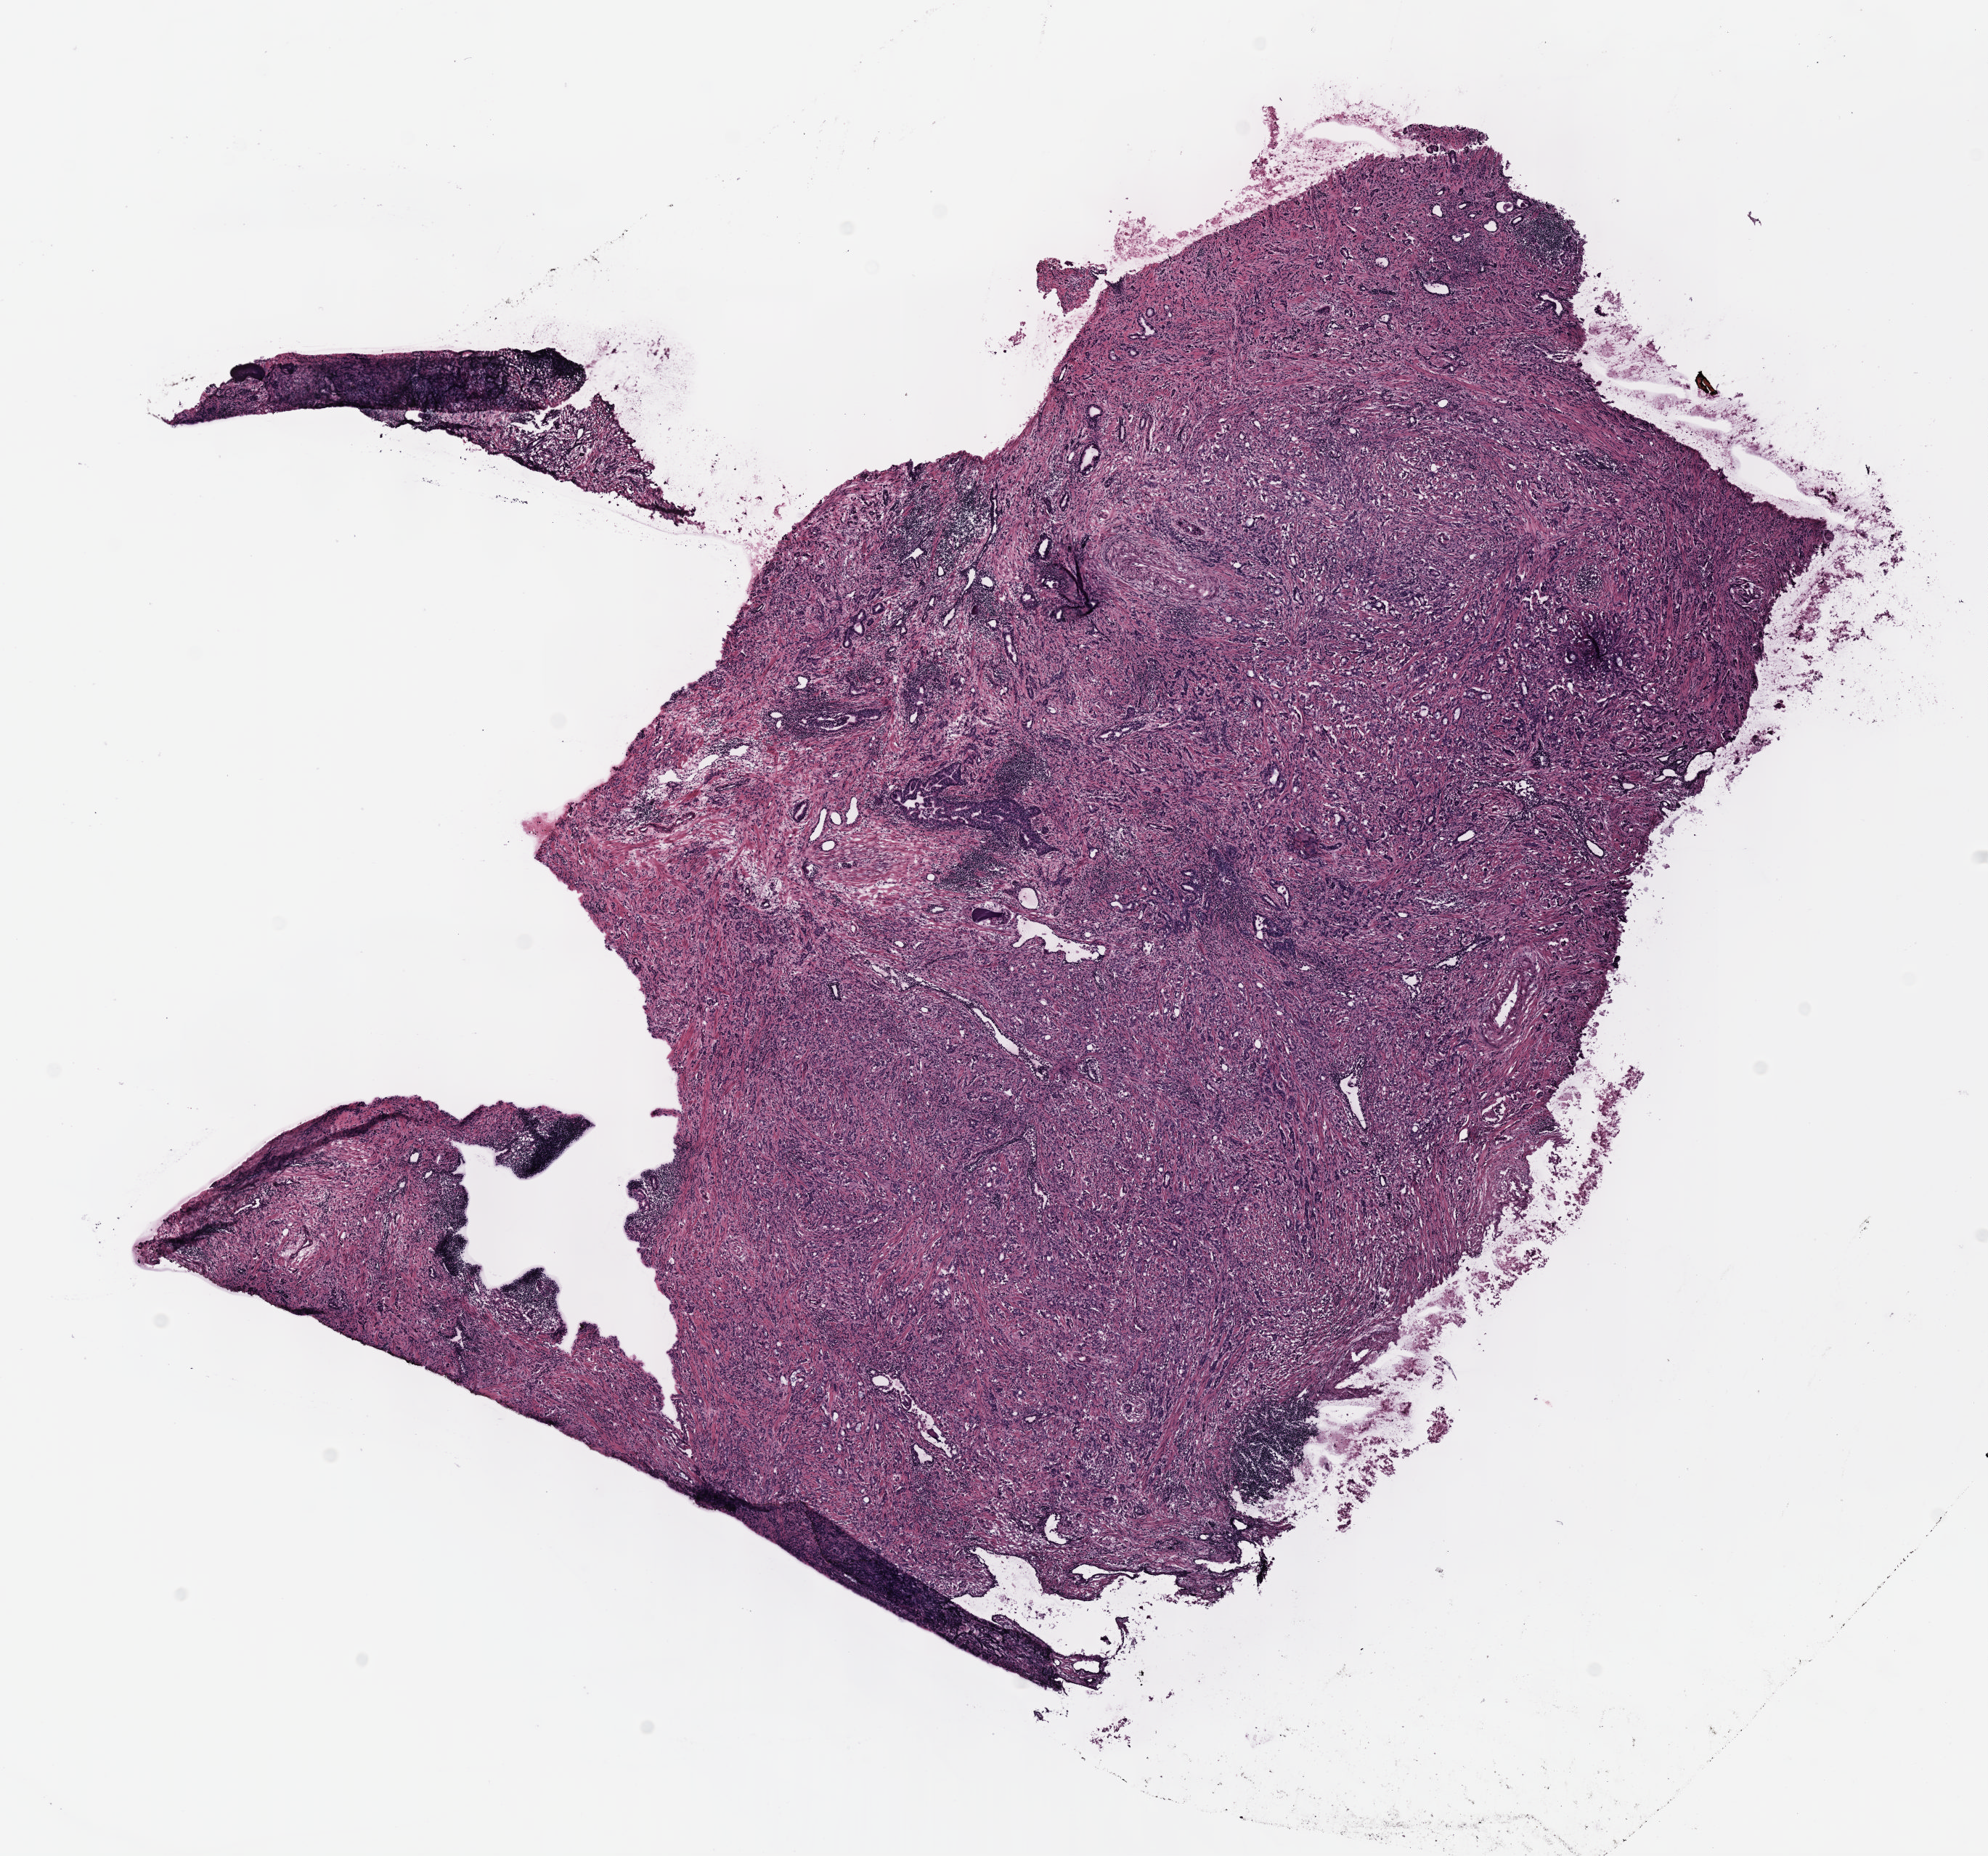
Whole-slide histology image, H&E-stained, a low-resolution overview of the entire scanned area, about 11.1 x 10.3 mm (acquisition: 40x scan). Frozen section from the top of the tissue portion. Primary tumour sample from the prostate. Patient: male, age at initial diagnosis 67 years. Gleason score: 7 (4+3). Pathologist review of this section (percent, as recorded): tumour cells 60%, tumour nuclei 65%, normal cells 10%, stromal cells 30%, necrosis 0%. Inflammatory infiltration, as recorded: lymphocyte infiltration 0%, monocyte infiltration 0%, neutrophil infiltration 0%.
Lymph nodes positive (case pathology): 0 of 12 examined. Diagnosis: Adenocarcinoma, NOS (prostate gland).